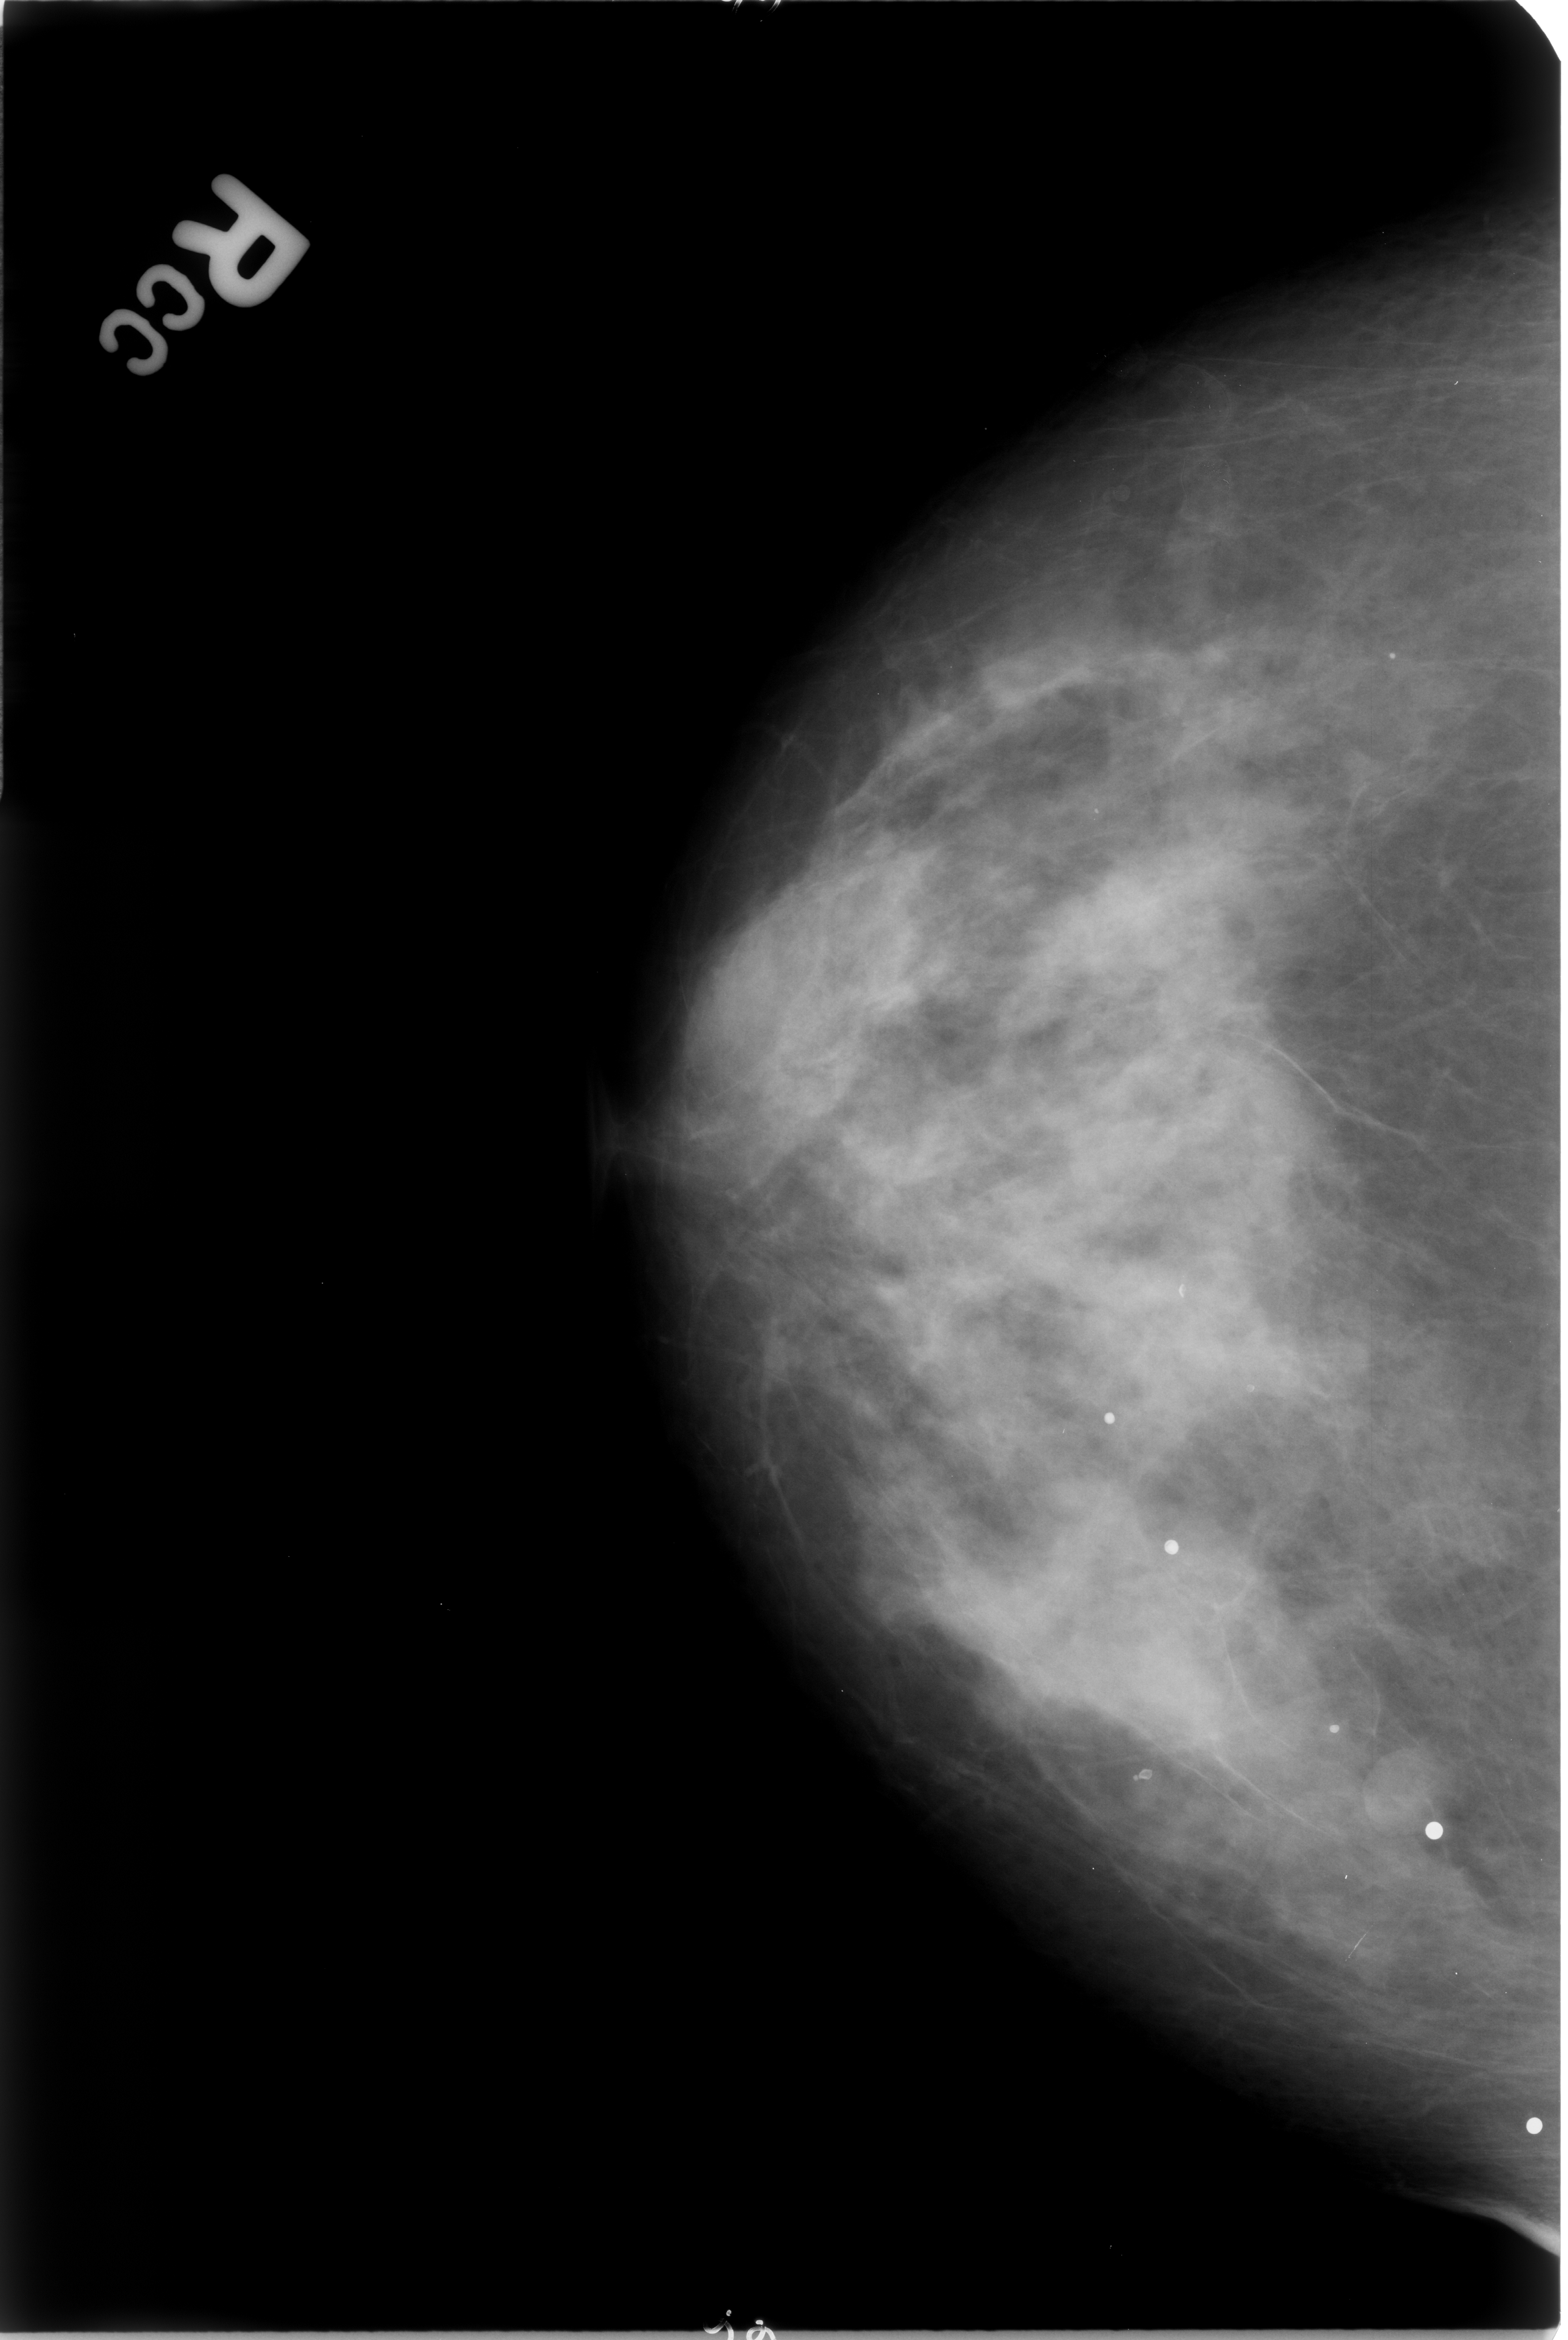
Scanned film-screen mammogram; right breast; CC view; BI-RADS breast density category 3 (scale 1–4).
Marked findings (only marked abnormalities are described; nothing is implied about the rest of the image): Finding 1 of 5: calcifications, morphology round and regular / lucent center; BI-RADS assessment category 2; subtlety rating 5 on a 1 (subtle) to 5 (obvious) scale; benign; no additional work-up was recommended (benign without callback). Finding 2 of 5: calcifications, morphology round and regular / lucent center; BI-RADS assessment category 2; benign; no additional work-up was recommended (benign without callback). Finding 3 of 5: calcifications, morphology round and regular / lucent center; BI-RADS assessment category 2; subtlety rating 5 on a 1 (subtle) to 5 (obvious) scale; benign; no additional work-up was recommended (benign without callback). Finding 4 of 5: calcifications, morphology round and regular / lucent center; BI-RADS assessment category 2; benign; no additional work-up was recommended (benign without callback). Finding 5 of 5: calcifications, morphology round and regular / lucent center; BI-RADS assessment category 2; subtlety rating 5 on a 1 (subtle) to 5 (obvious) scale; benign without callback (not worked up further).